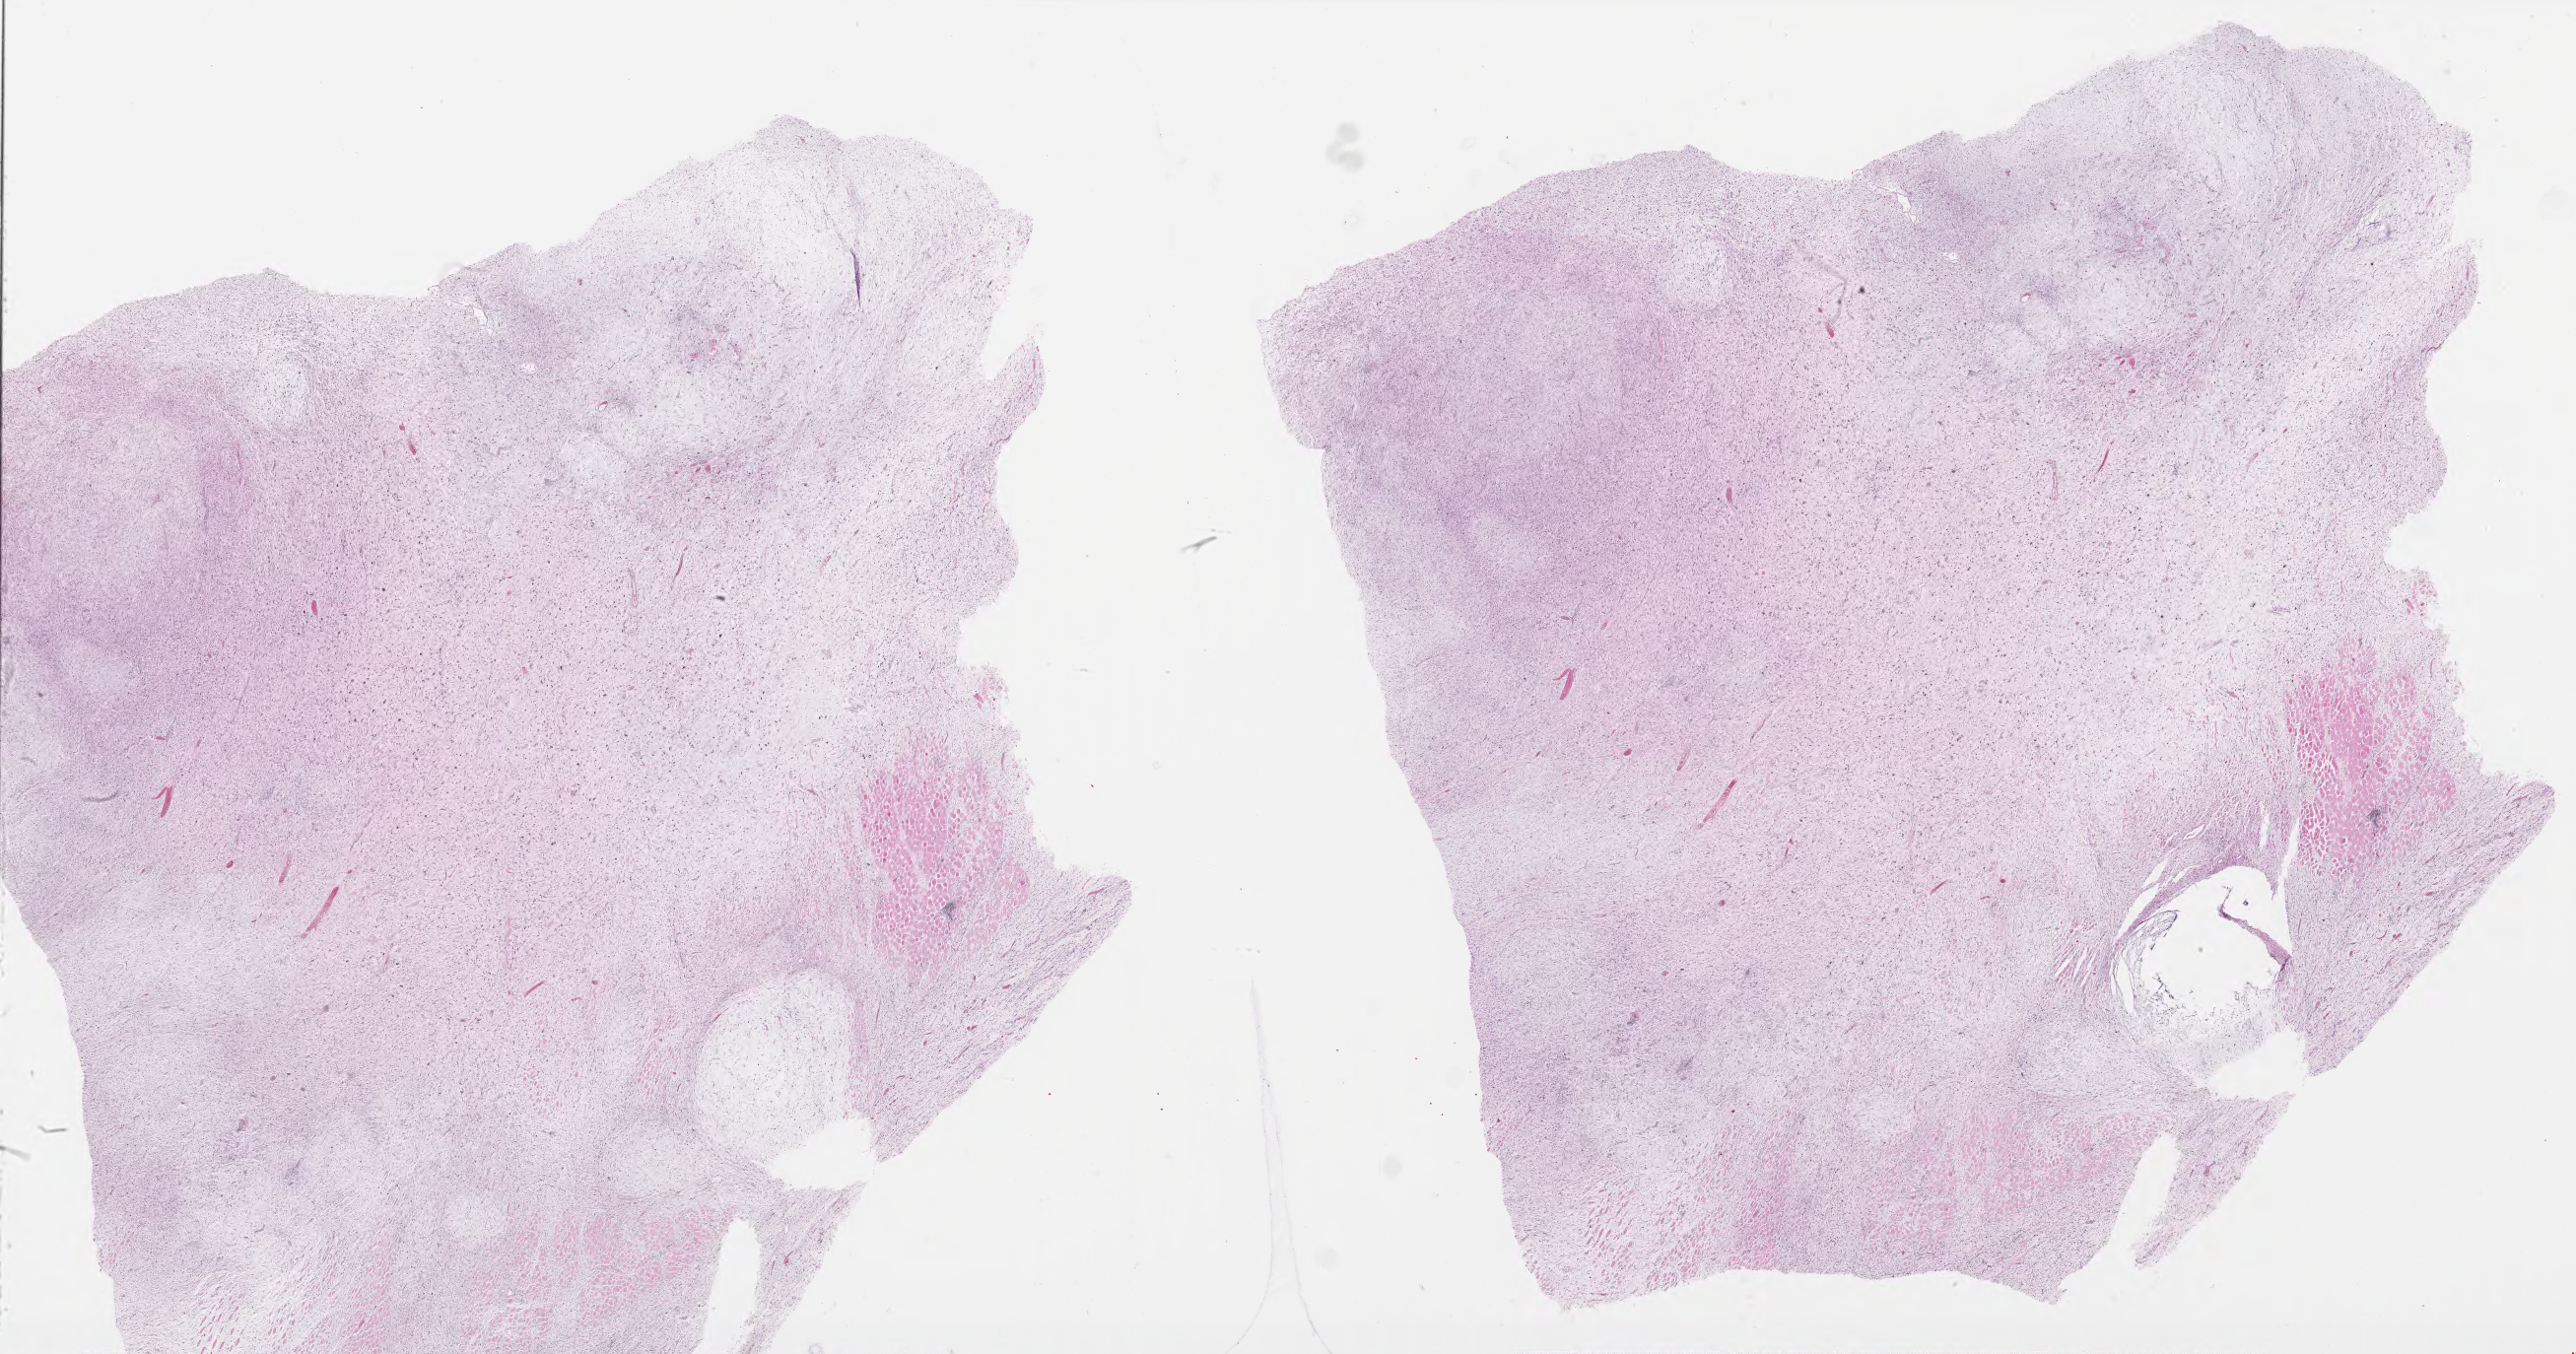
H&E whole-slide image, whole scanned area (about 42.0 x 22.1 mm, acquisition: 40x scan) shown as a low-resolution overview, formalin-fixed paraffin-embedded (FFPE) diagnostic section, primary tumour sample from the connective, subcutaneous and other soft tissues. Male, age 75 years at initial diagnosis.
* histologic diagnosis: Fibromyxosarcoma (connective, subcutaneous and other soft tissues of thorax)